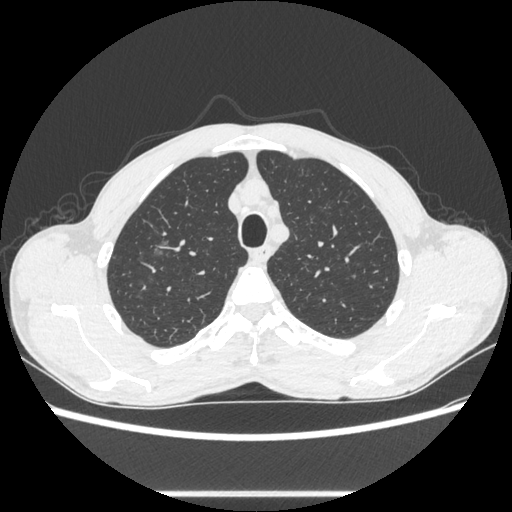
Chest CT, one axial slice. Slice 475 of 600 in the series (ordered by position). Reconstruction kernel STANDARD. Lung window (W 1500 / L -600 HU). 0.62 mm slice thickness. 512 × 512 image matrix, field of view 357 × 357 mm. Patient: male, 54 years. From the clinical record (not read from this slice): clinical TNM (as recorded): T1a N0 M0.
Outlined on this slice (rectangle marked by the reading radiologist):
- lung tumour (recorded histology: adenocarcinoma): box from (x=149, y=234) to (x=176, y=256) px